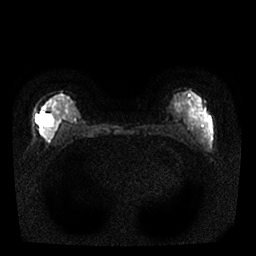
Breast MRI, one axial slice. Slice 10 of 25 in the series (ordered by position). Diffusion-weighted series; image 2 of 4 stored at this slice position (different b-values; order by instance number). 1.5 T. 4 mm slice thickness. 256 × 256 image matrix, field of view 310 × 310 mm. Female patient.
Annotated regions visible in this slice (outlined manually by an expert reader):
- tumour on diffusion-weighted imaging: box from (x=37, y=112) to (x=58, y=140) px